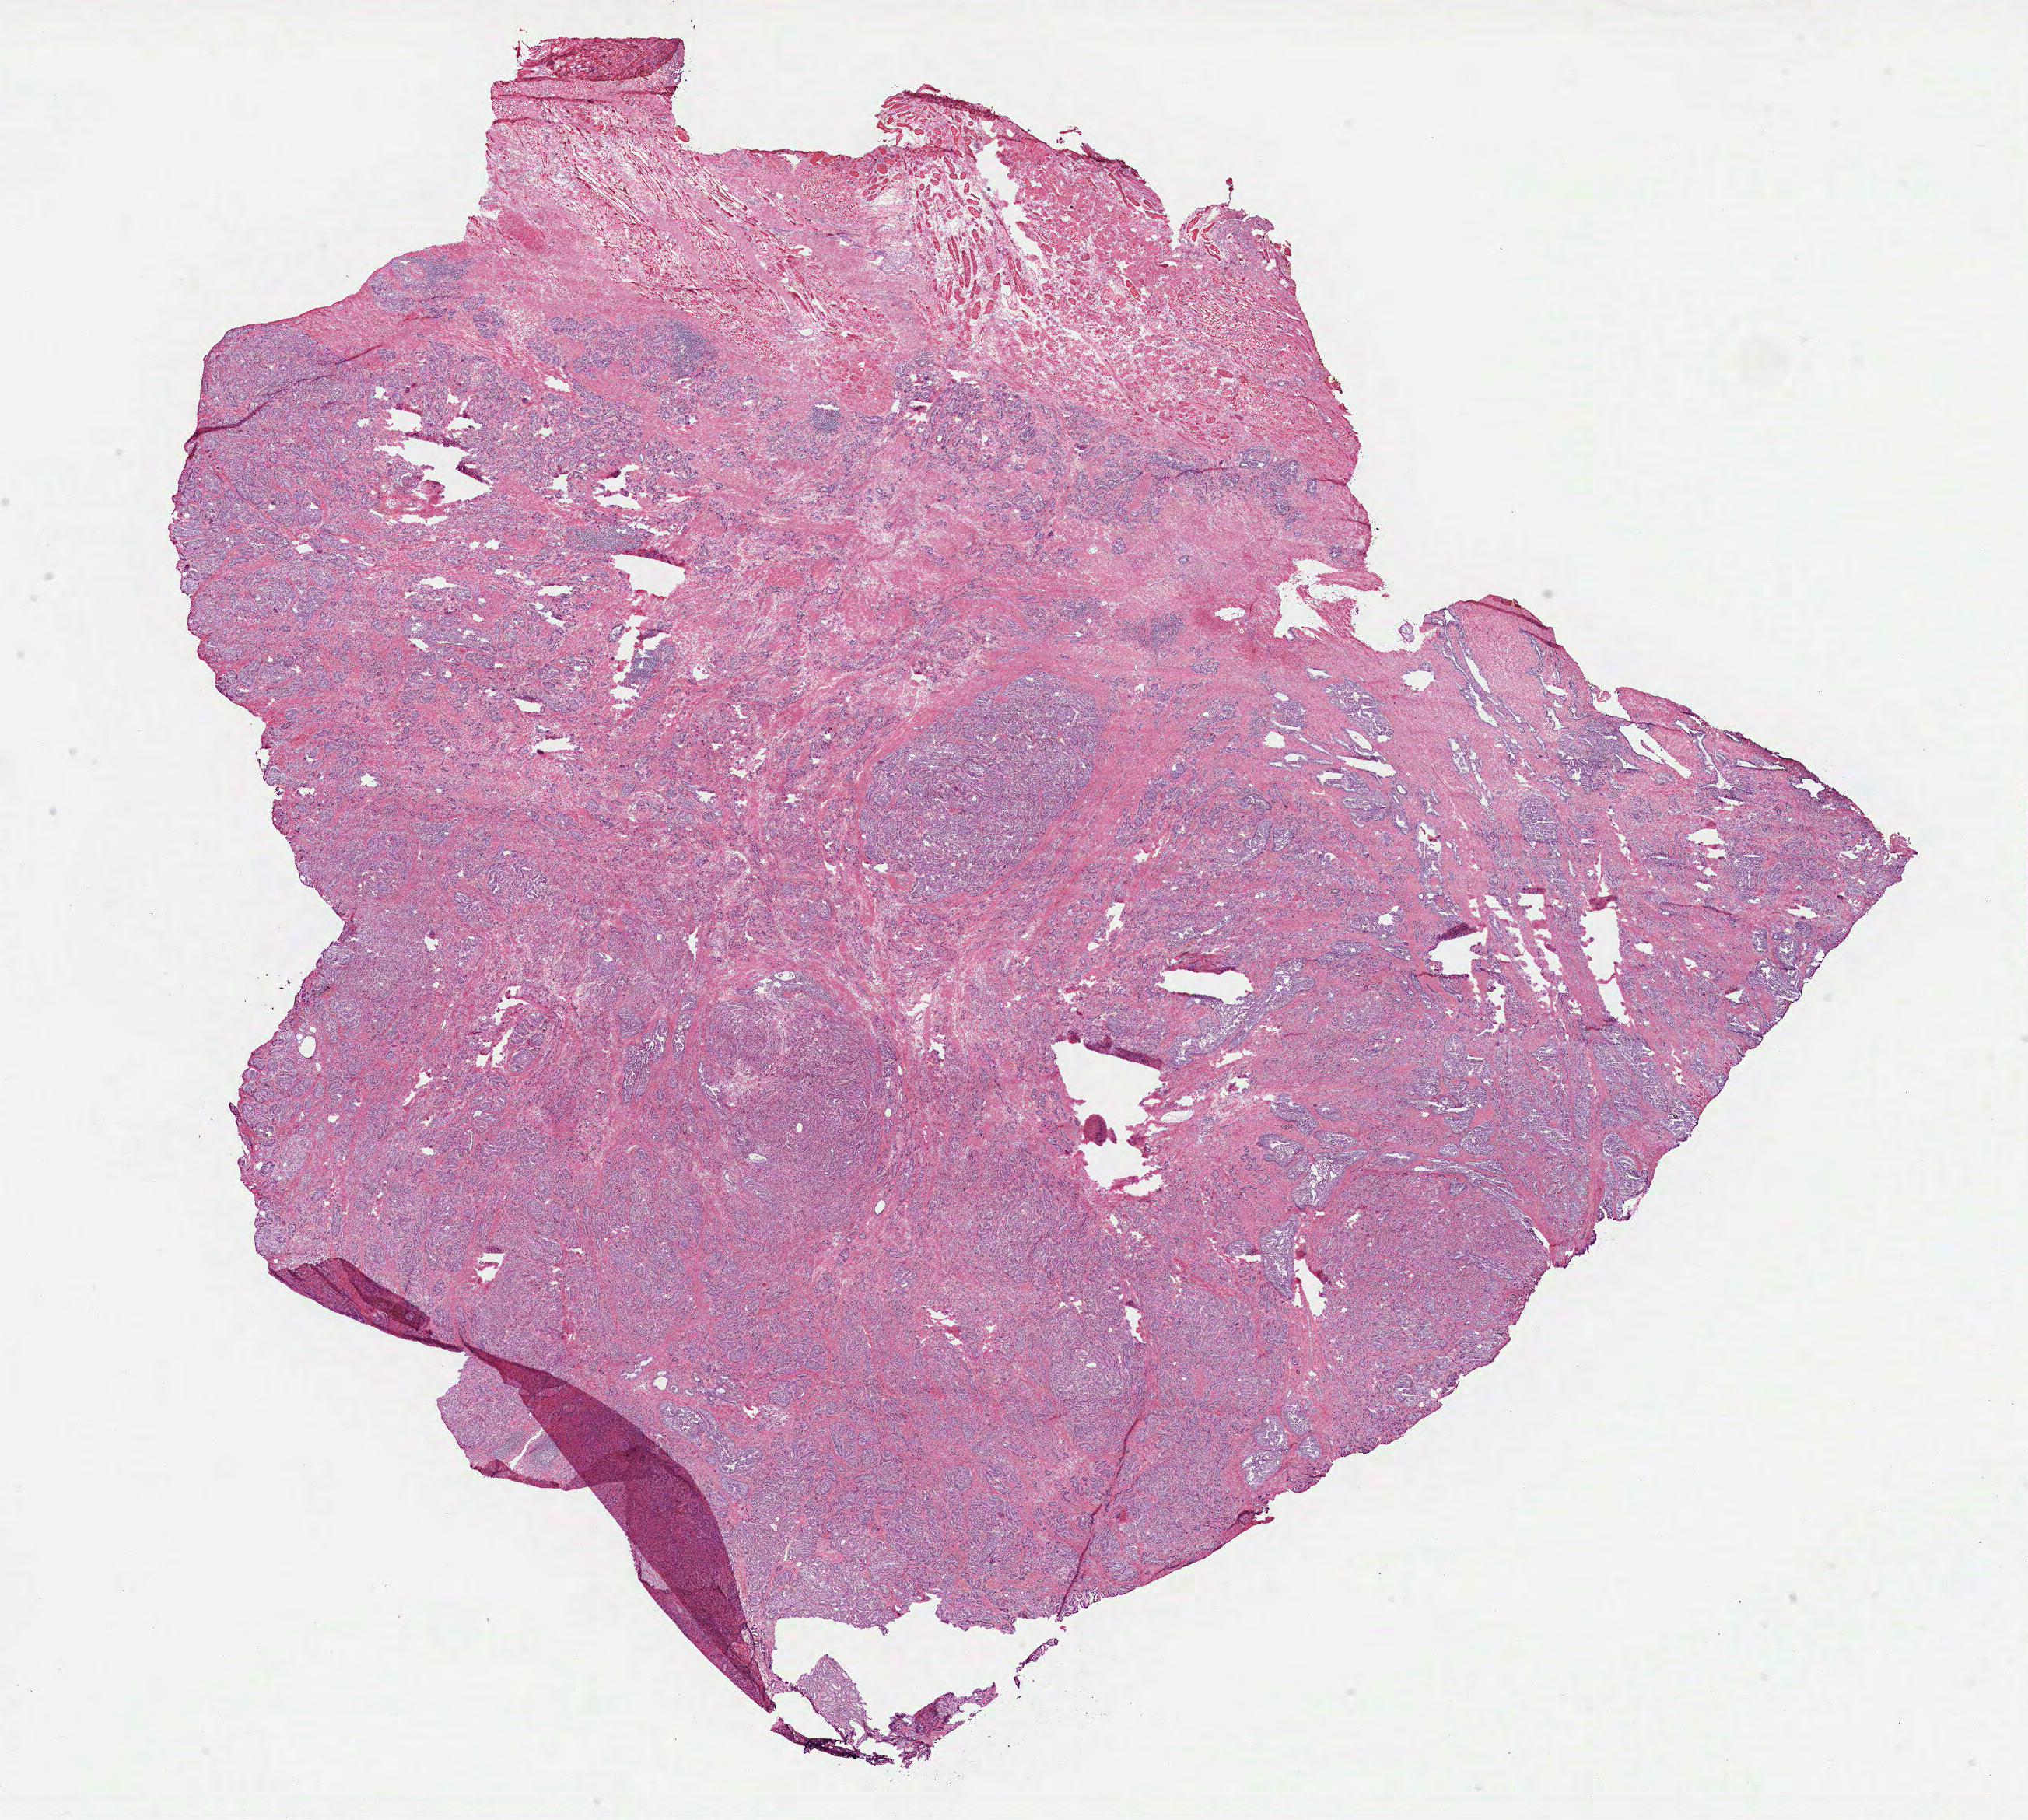
Hematoxylin and eosin (H&E) stained whole-slide image, shown as a low-resolution overview of the whole scanned area (about 21.0 x 18.9 mm, slide scanned at 40x); frozen section from the top of the tissue portion; sample: primary tumour, prostate. Male patient; age at initial diagnosis 53 years. Gleason score: 7 (3+4). Pathologist review of this section (percent, as recorded): tumour cells 90%, tumour nuclei 95%, normal cells 2%, stromal cells 8%, necrosis 0%. Inflammatory infiltration, as recorded: lymphocyte infiltration 2%, monocyte infiltration 0%, neutrophil infiltration 0%.
Lymph nodes positive (case pathology): 0 of 6 examined. Diagnosis: Acinar cell carcinoma (prostate gland).